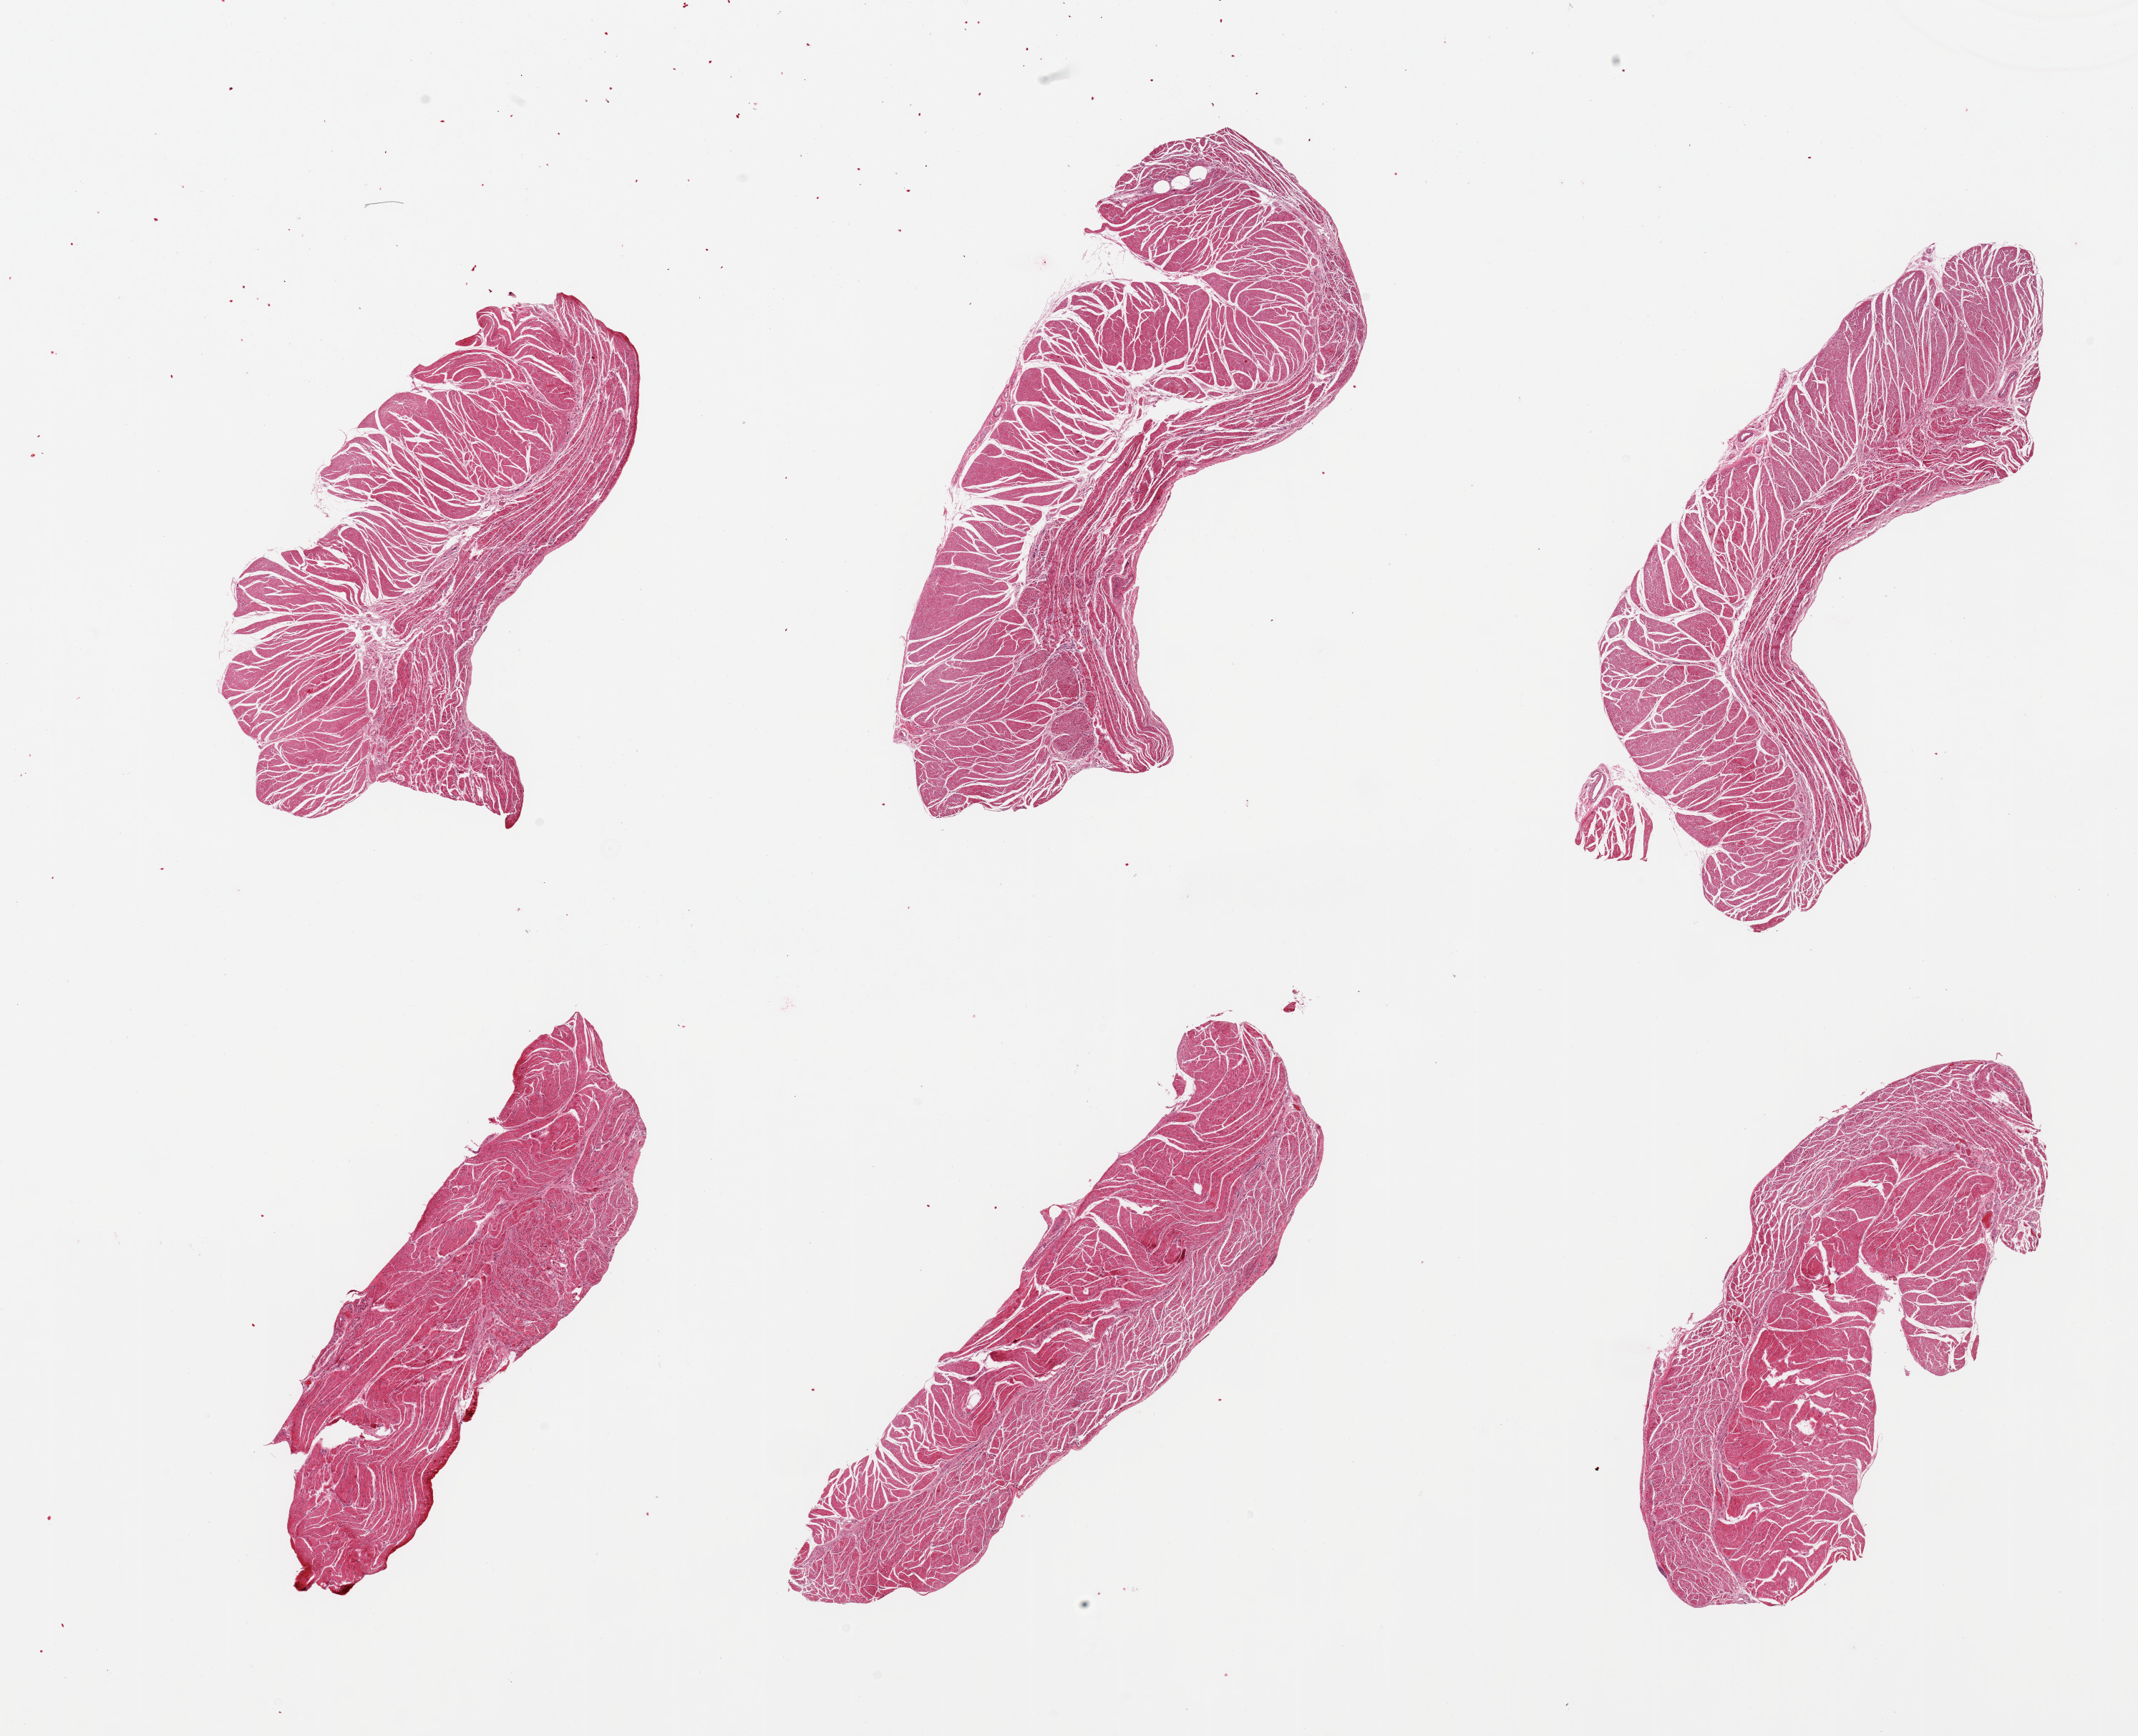
Whole-slide image, H&E stain, brightfield — shown as a low-resolution overview of the whole scanned area (about 23.6 x 19.2 mm); PAXgene-fixed paraffin-embedded (PFPE) section; target tissue: esophageal muscle; donor tissue sample. Donor: female.
Reviewer comment on this tissue sample: 6 pieces, confirmed target muscularis.